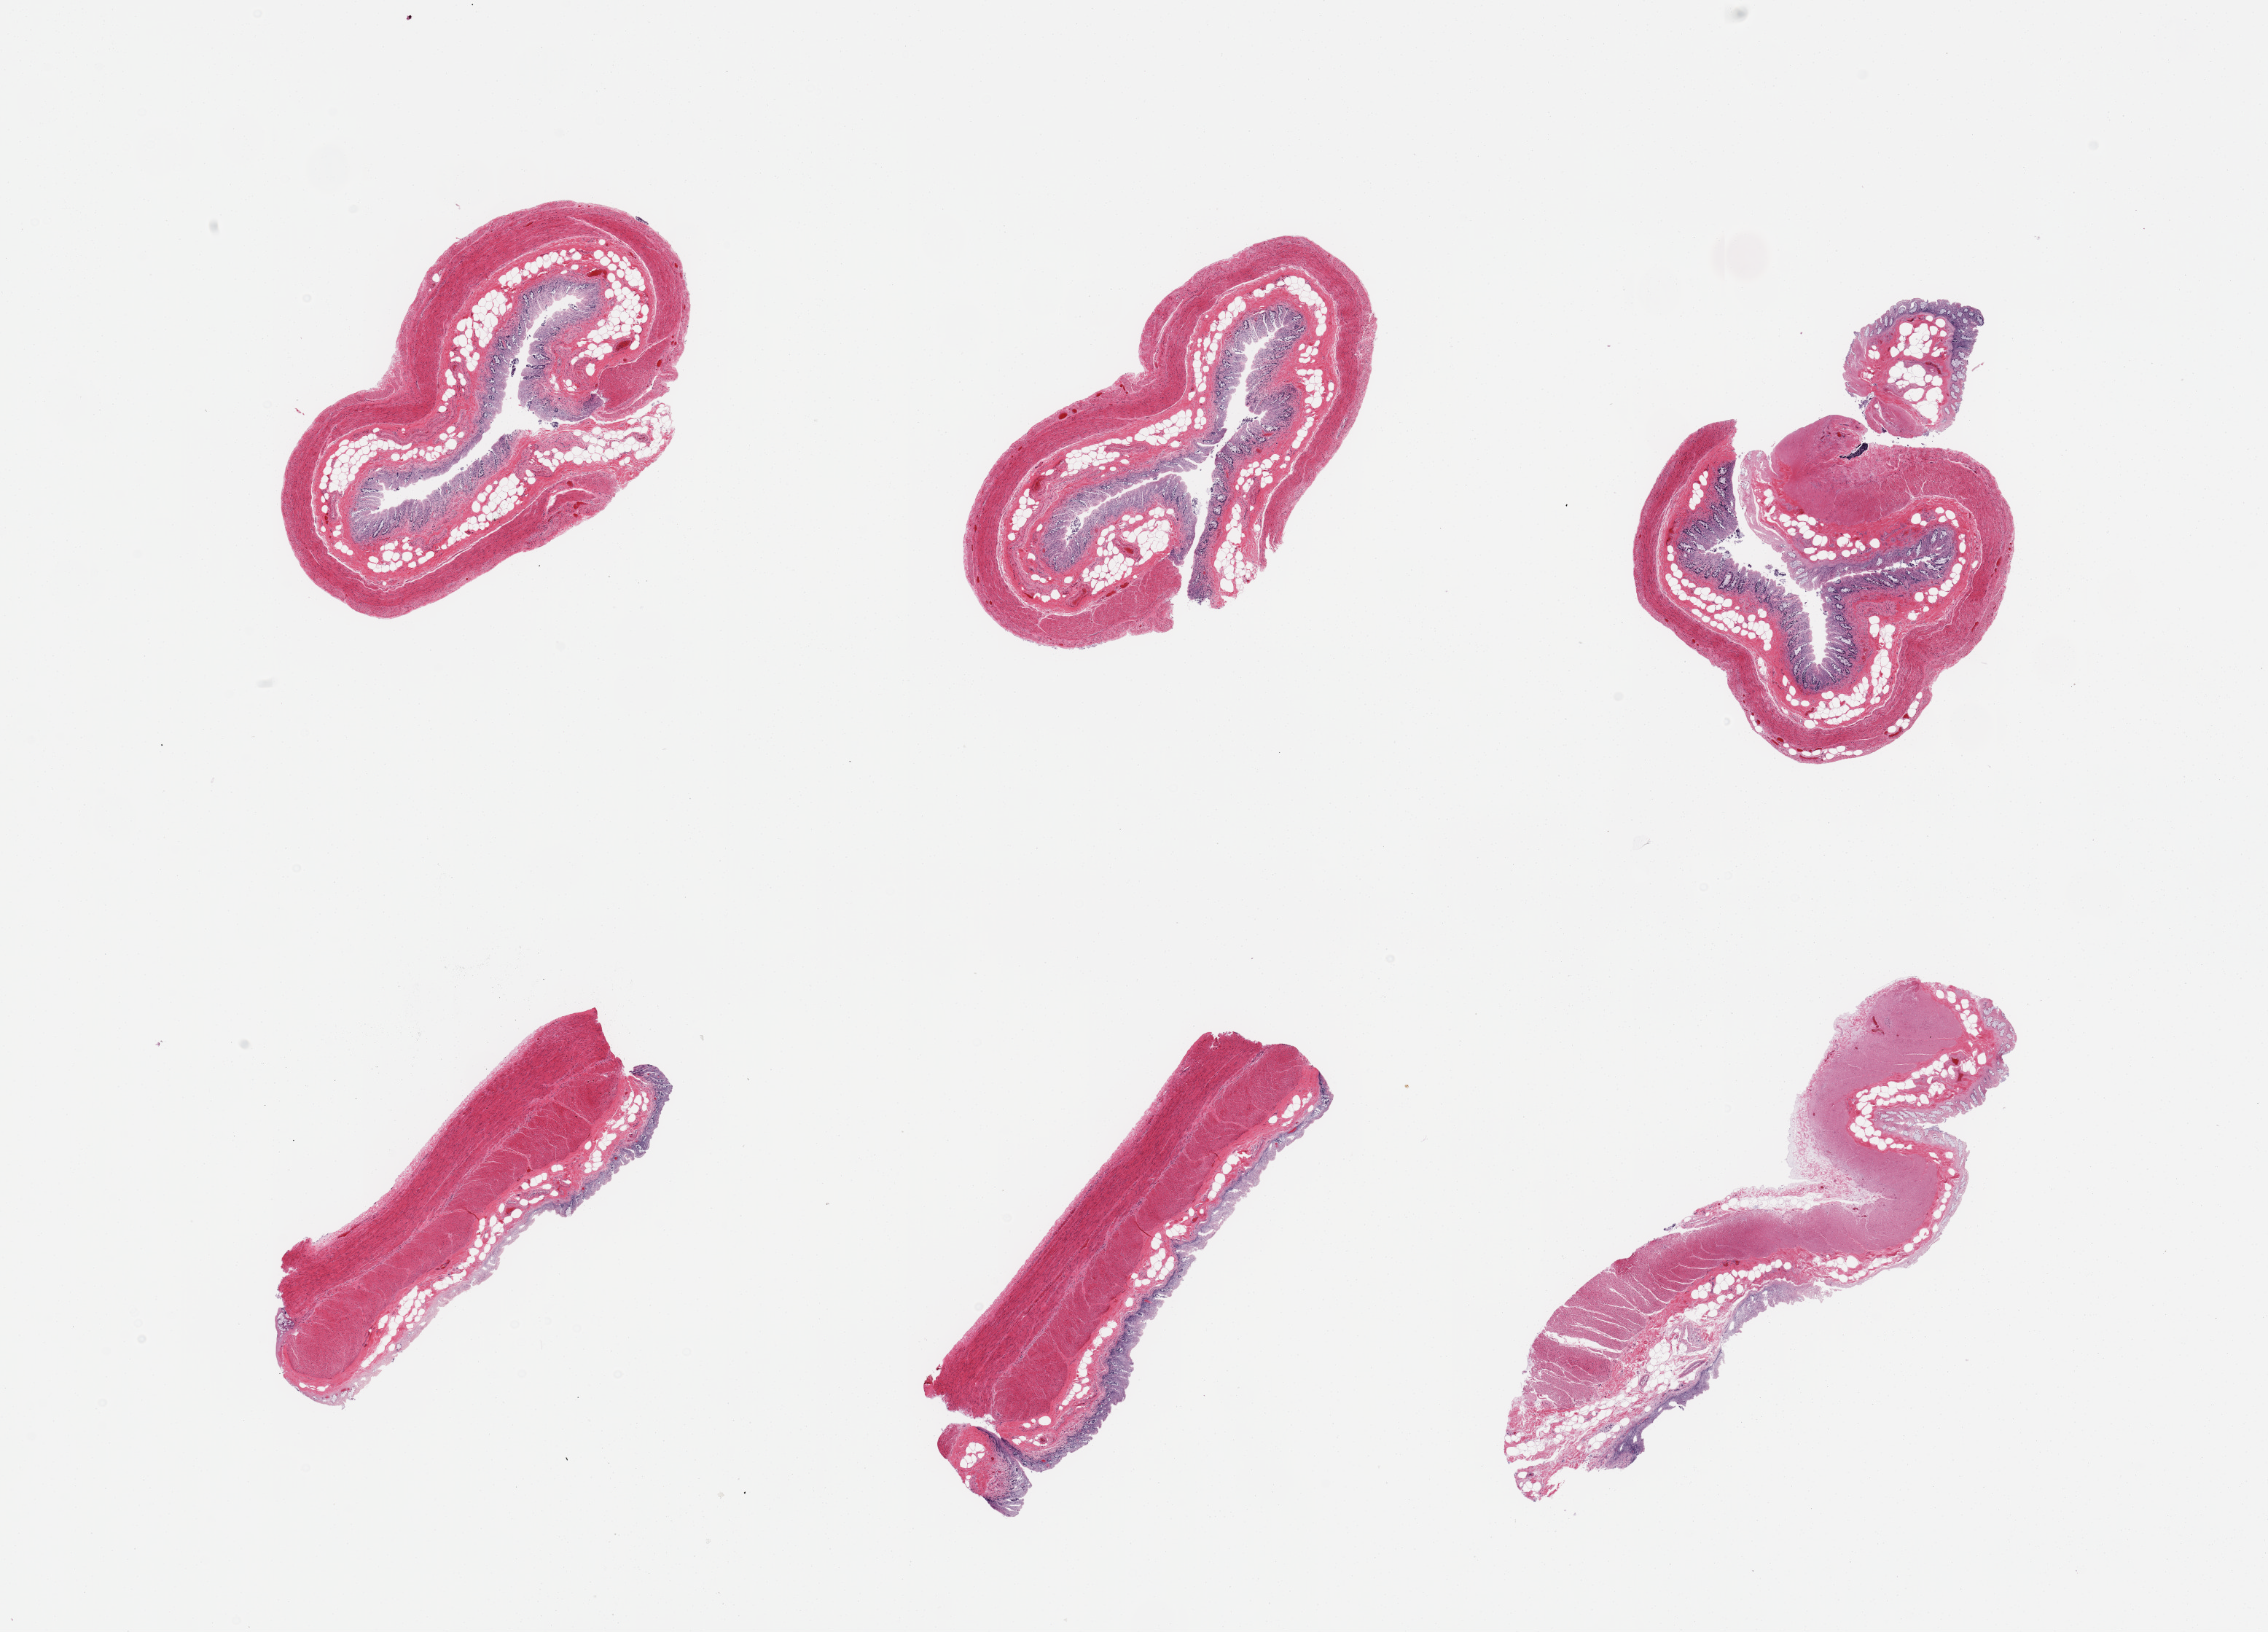
Whole-slide image, H&E stain, shown as a low-resolution overview of the whole scanned area (about 24.6 x 17.7 mm); PAXgene-fixed, paraffin-embedded tissue; sampled site (target tissue): transverse colon; tissue donor sample. Donor: male.
Reviewer comment on this tissue sample: 6 pieces; severely autolyzed mucosa and preserved muscularis; congestion.